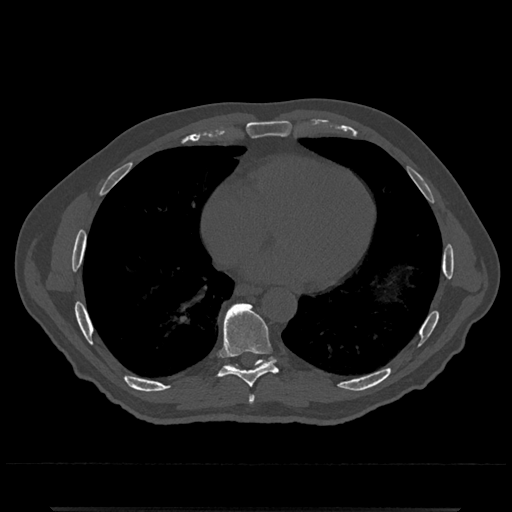
CT including the spine, one axial slice. Position 661 of 797 along the scan axis. Reconstruction kernel Br40s/3. 120 kVp. Bone window (W 1800 / L 400 HU). 0.5 mm slice thickness. 512 × 512 image matrix, field of view 393 × 393 mm. Male patient, age 67 years. From the clinical record (not read from this slice): primary cancer: prostate.
Annotated regions visible in this slice (semi-automatically segmented with operator editing):
- T7 vertebra: box from (x=248, y=395) to (x=255, y=404) px
- T8 vertebra: (x=217, y=303)–(x=278, y=388)
- T9 vertebra: (x=225, y=357)–(x=276, y=369)